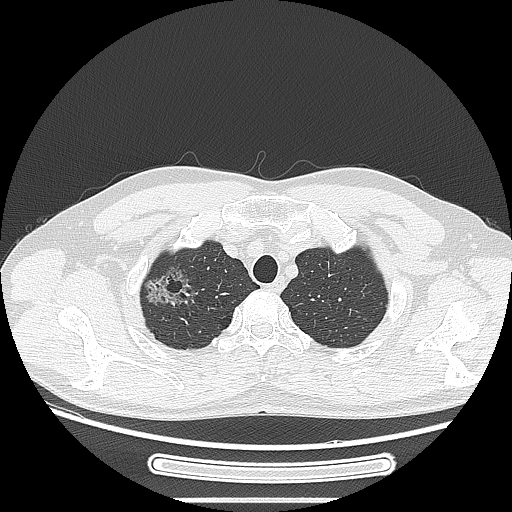
Chest CT, one axial slice; slice 228 of 269 in the series (ordered by position); reconstruction kernel LUNG; lung window (W 1500 / L -600 HU); 1.25 mm slice thickness; 512 × 512 image matrix, field of view 382 × 382 mm. Male patient, age 53 years. From the clinical record (not read from this slice): clinical TNM (as recorded): T1c N0 M0; histopathological grade: G2.
Annotated regions visible in this slice (bounding box drawn by a radiologist):
- lung tumour (recorded histology: adenocarcinoma): bounding box [x1, y1, x2, y2] px = [145, 262, 195, 315]